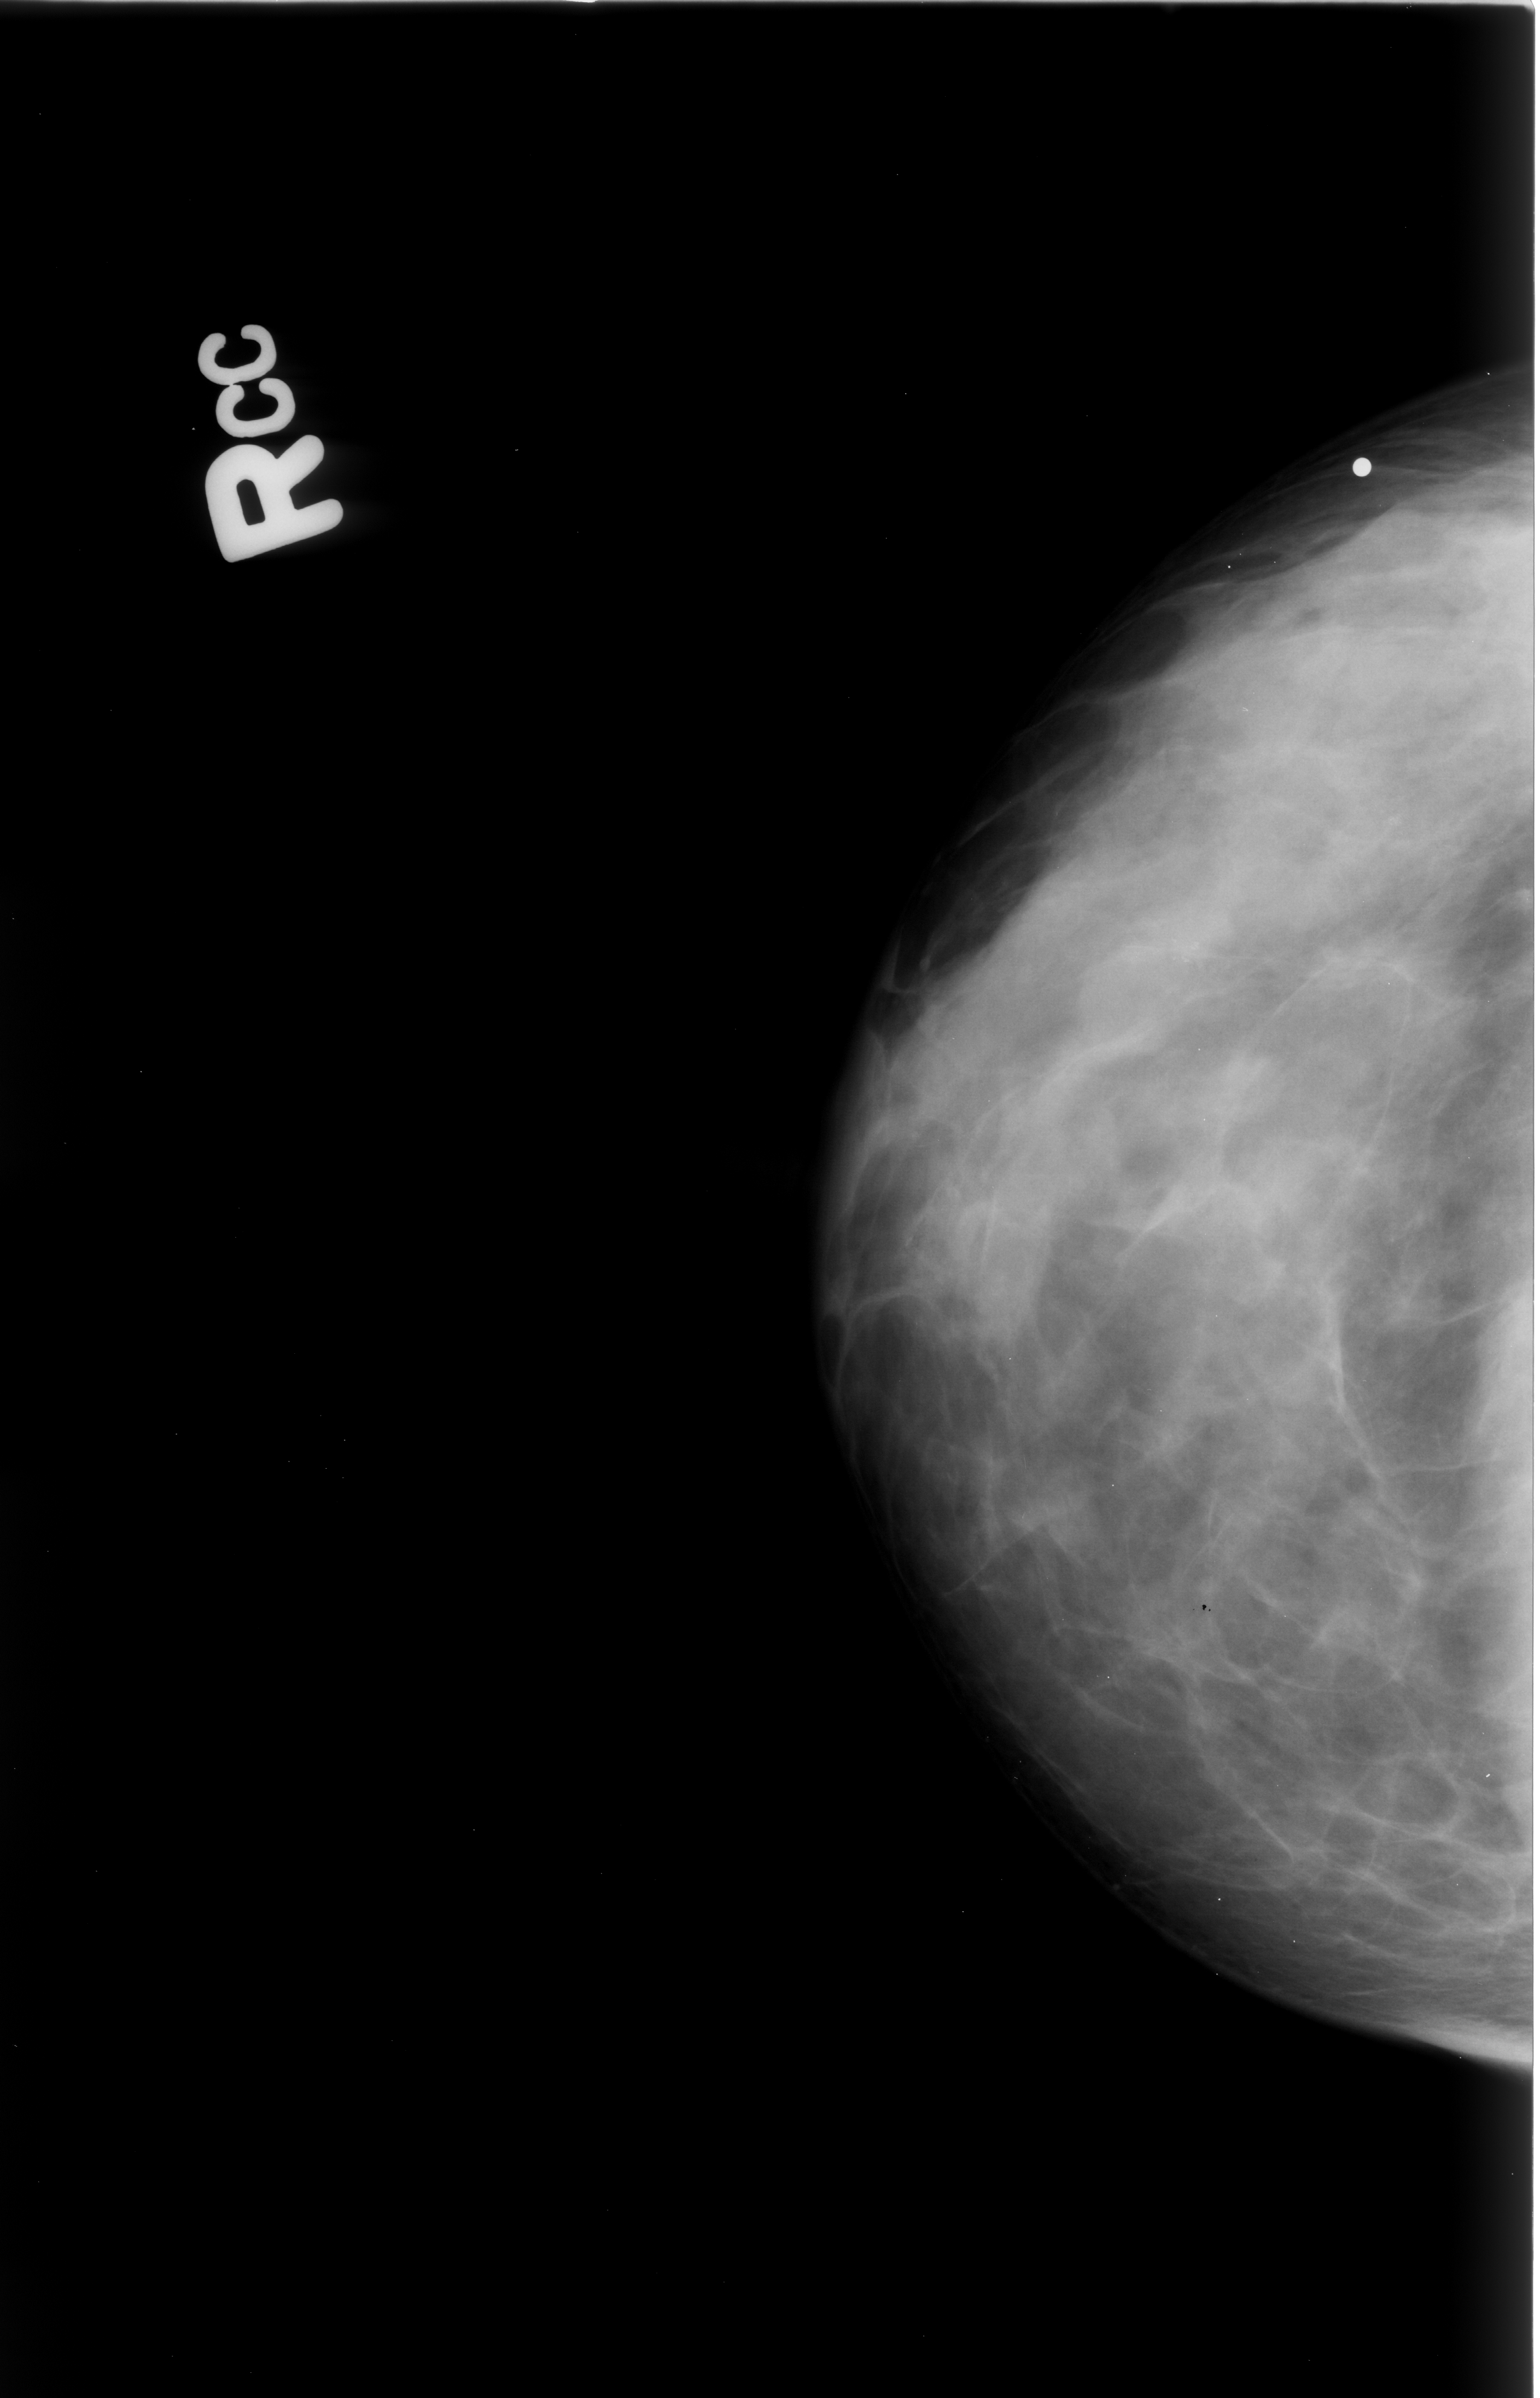
Mammogram (digitized film). Right breast. CC view. 1540 × 2398 image matrix.
Expert-marked regions of interest on this film, with their recorded descriptors:
- calcifications, morphology pleomorphic, distribution clustered; BI-RADS assessment category 4; pathology (as recorded): benign: bounding box <1071,901,1287,1056> (left, top, right, bottom; pixels)